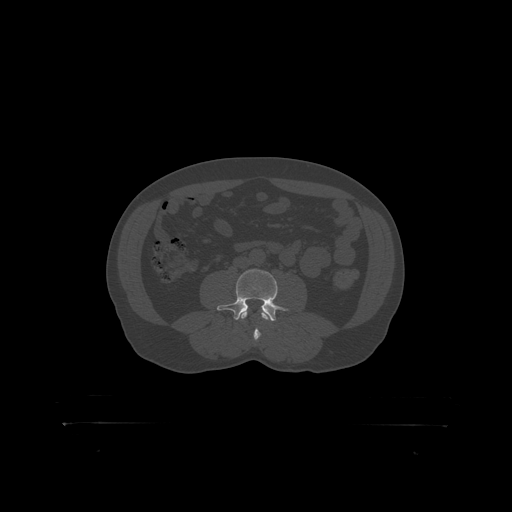
CT including the spine, one axial slice. Slice 245 of 399 in the series (ordered by position). Bone window (W 1800 / L 400 HU). 1.25 mm slice thickness. 512 × 512 image matrix, field of view 650 × 650 mm. Patient: male, 46 years. Case-level facts recorded for this patient, not image findings: primary cancer: skin.
Outlined on this slice (semi-automatically segmented with operator editing):
- L3 vertebra: bounding box (x1, y1, x2, y2) in pixels: (241, 312, 268, 319)
- L4 vertebra: (219, 269, 288, 318)